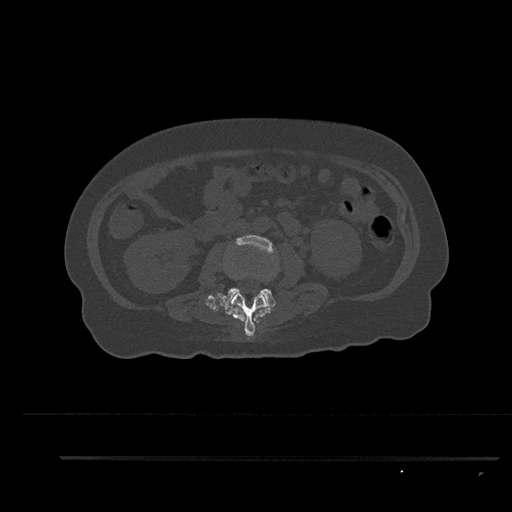
CT including the spine, one axial slice; slice 122 of 797 in the series (ordered by position); 120 kVp; bone window (W 1800 / L 400 HU); 0.5 mm slice thickness; 512 × 512 image matrix, field of view 408 × 408 mm. Patient: female, 44 years. From the clinical record (not read from this slice): primary cancer: renal; vertebrae with lytic lesions (as recorded): L1.
Annotated regions visible in this slice (semi-automatic segmentation, software-assisted and operator-edited):
- L2 vertebra: bounding box <226,292,269,337> (left, top, right, bottom; pixels)
- L3 vertebra: <223,235,279,308>